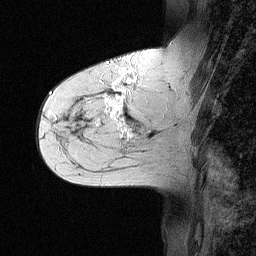
Breast MRI (dynamic contrast-enhanced), one sagittal slice; position 24 of 64 along the scan axis; dynamic contrast-enhanced study with each time point stored as its own series, time point 2 of 3 at this slice position (early post-contrast, ordered by acquisition time); 1.5 T; TE 4.5 ms, TR 11 ms; 2.06 mm slice thickness; 256 × 256 image matrix, field of view 200 × 200 mm. Patient: female, 55 years. Case-level facts recorded for this patient, not image findings: setting: breast cancer imaged before/during neoadjuvant chemotherapy; receptor status: triple-negative.
Structures marked on this image (semi-automatic segmentation, software-assisted and operator-edited):
- analysis volume of interest (the breast-tissue region the enhancement analysis was run in; not a lesion): bounding box (x1, y1, x2, y2) in pixels: (71, 63, 147, 145)
- tumour enhancement mask (voxels above the 90 % enhancement threshold inside the analysis volume of interest): (97, 69, 136, 125)